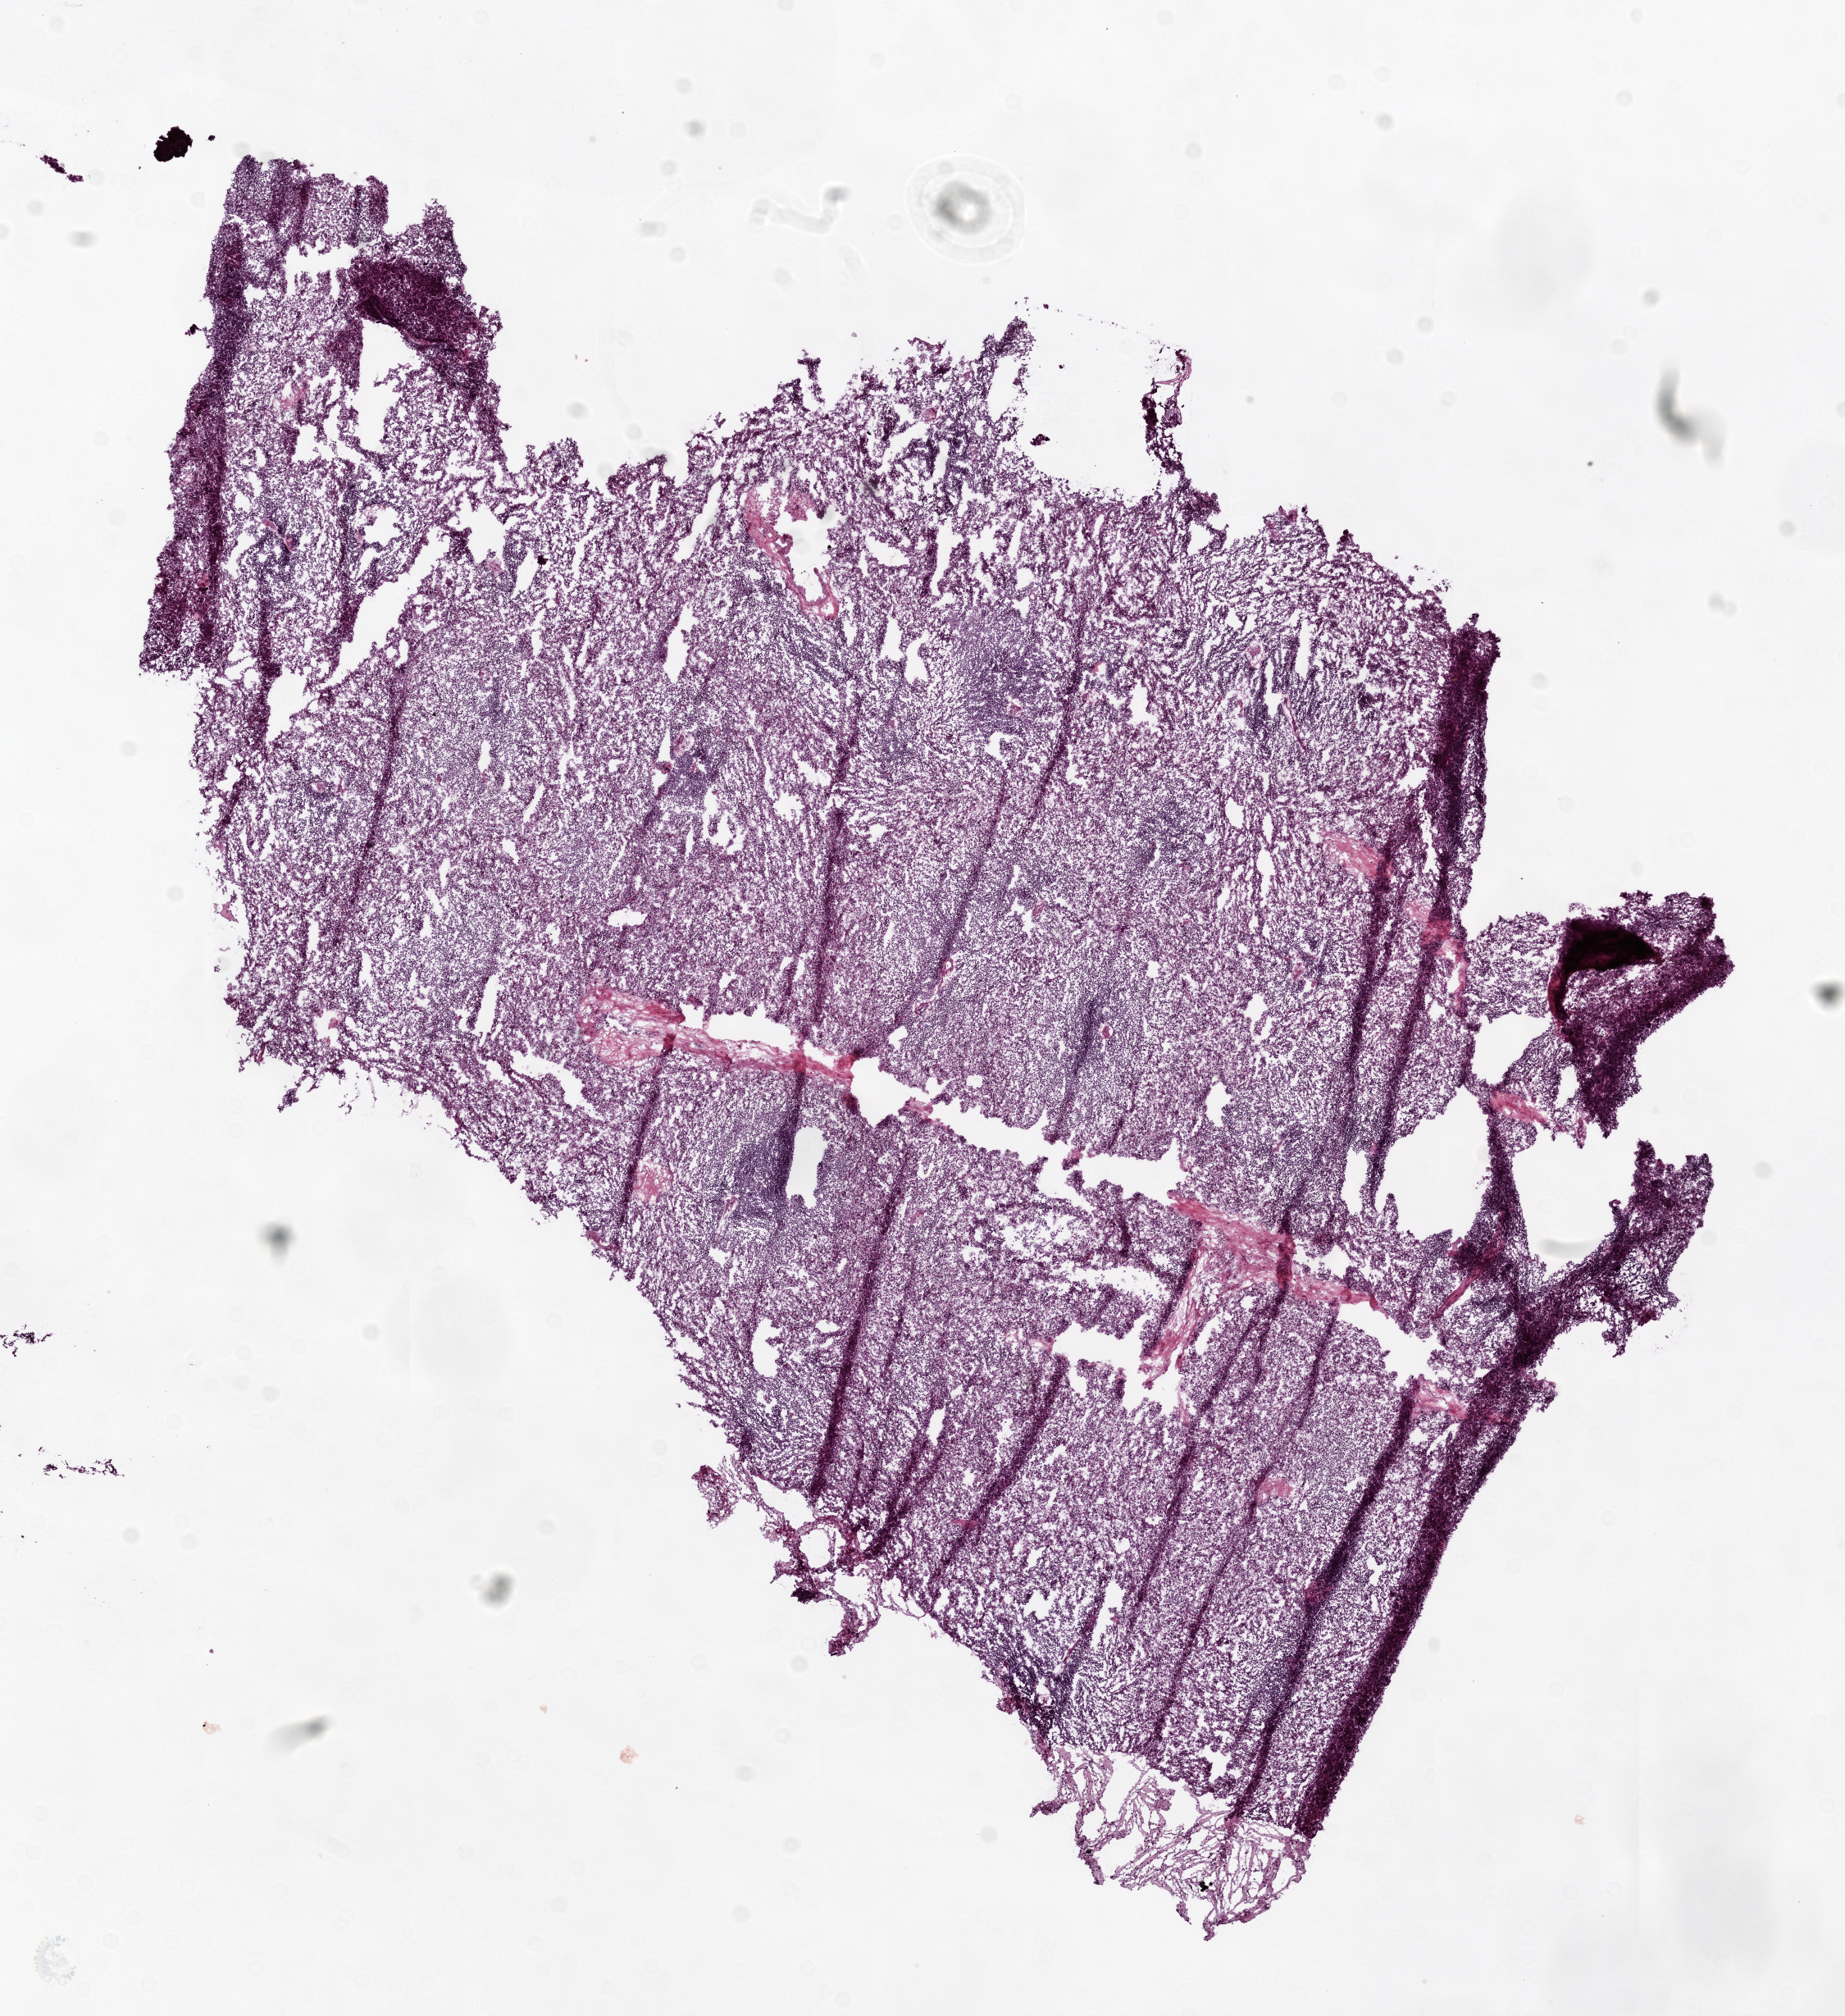
H&E-stained whole-slide image — a low-resolution overview of the entire scanned area, about 9.0 x 9.9 mm (acquisition: 20x scan), frozen section, ovary, solid tissue normal (non-tumour tissue) sample. Female, age 59 years at initial diagnosis.
This section: solid tissue normal sample (biorepository sample class). Patient diagnosis: Serous cystadenocarcinoma, NOS.